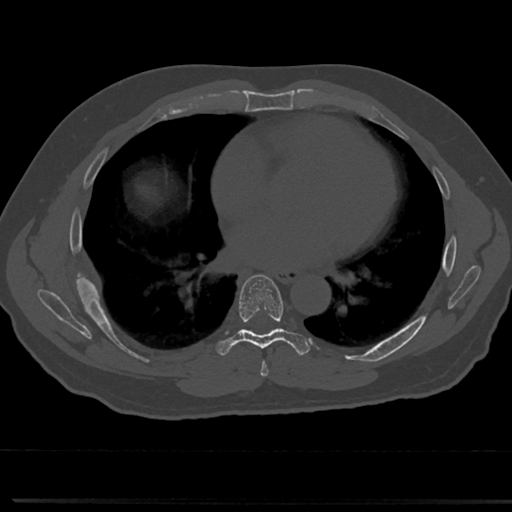
CT including the spine, one axial slice. Slice 408 of 817 in the series (ordered by position). Reconstruction kernel Br40s/3. 120 kVp. Bone window (W 1800 / L 400 HU). 0.5 mm slice thickness. 512 × 512 image matrix. Patient: male, 61 years. From the clinical record (not read from this slice): primary cancer: prostate.
Annotated regions visible in this slice (semi-automatic segmentation, software-assisted and operator-edited):
- T6 vertebra: box from (x=256, y=340) to (x=319, y=370) px
- T7 vertebra: (x=216, y=275)–(x=307, y=358)